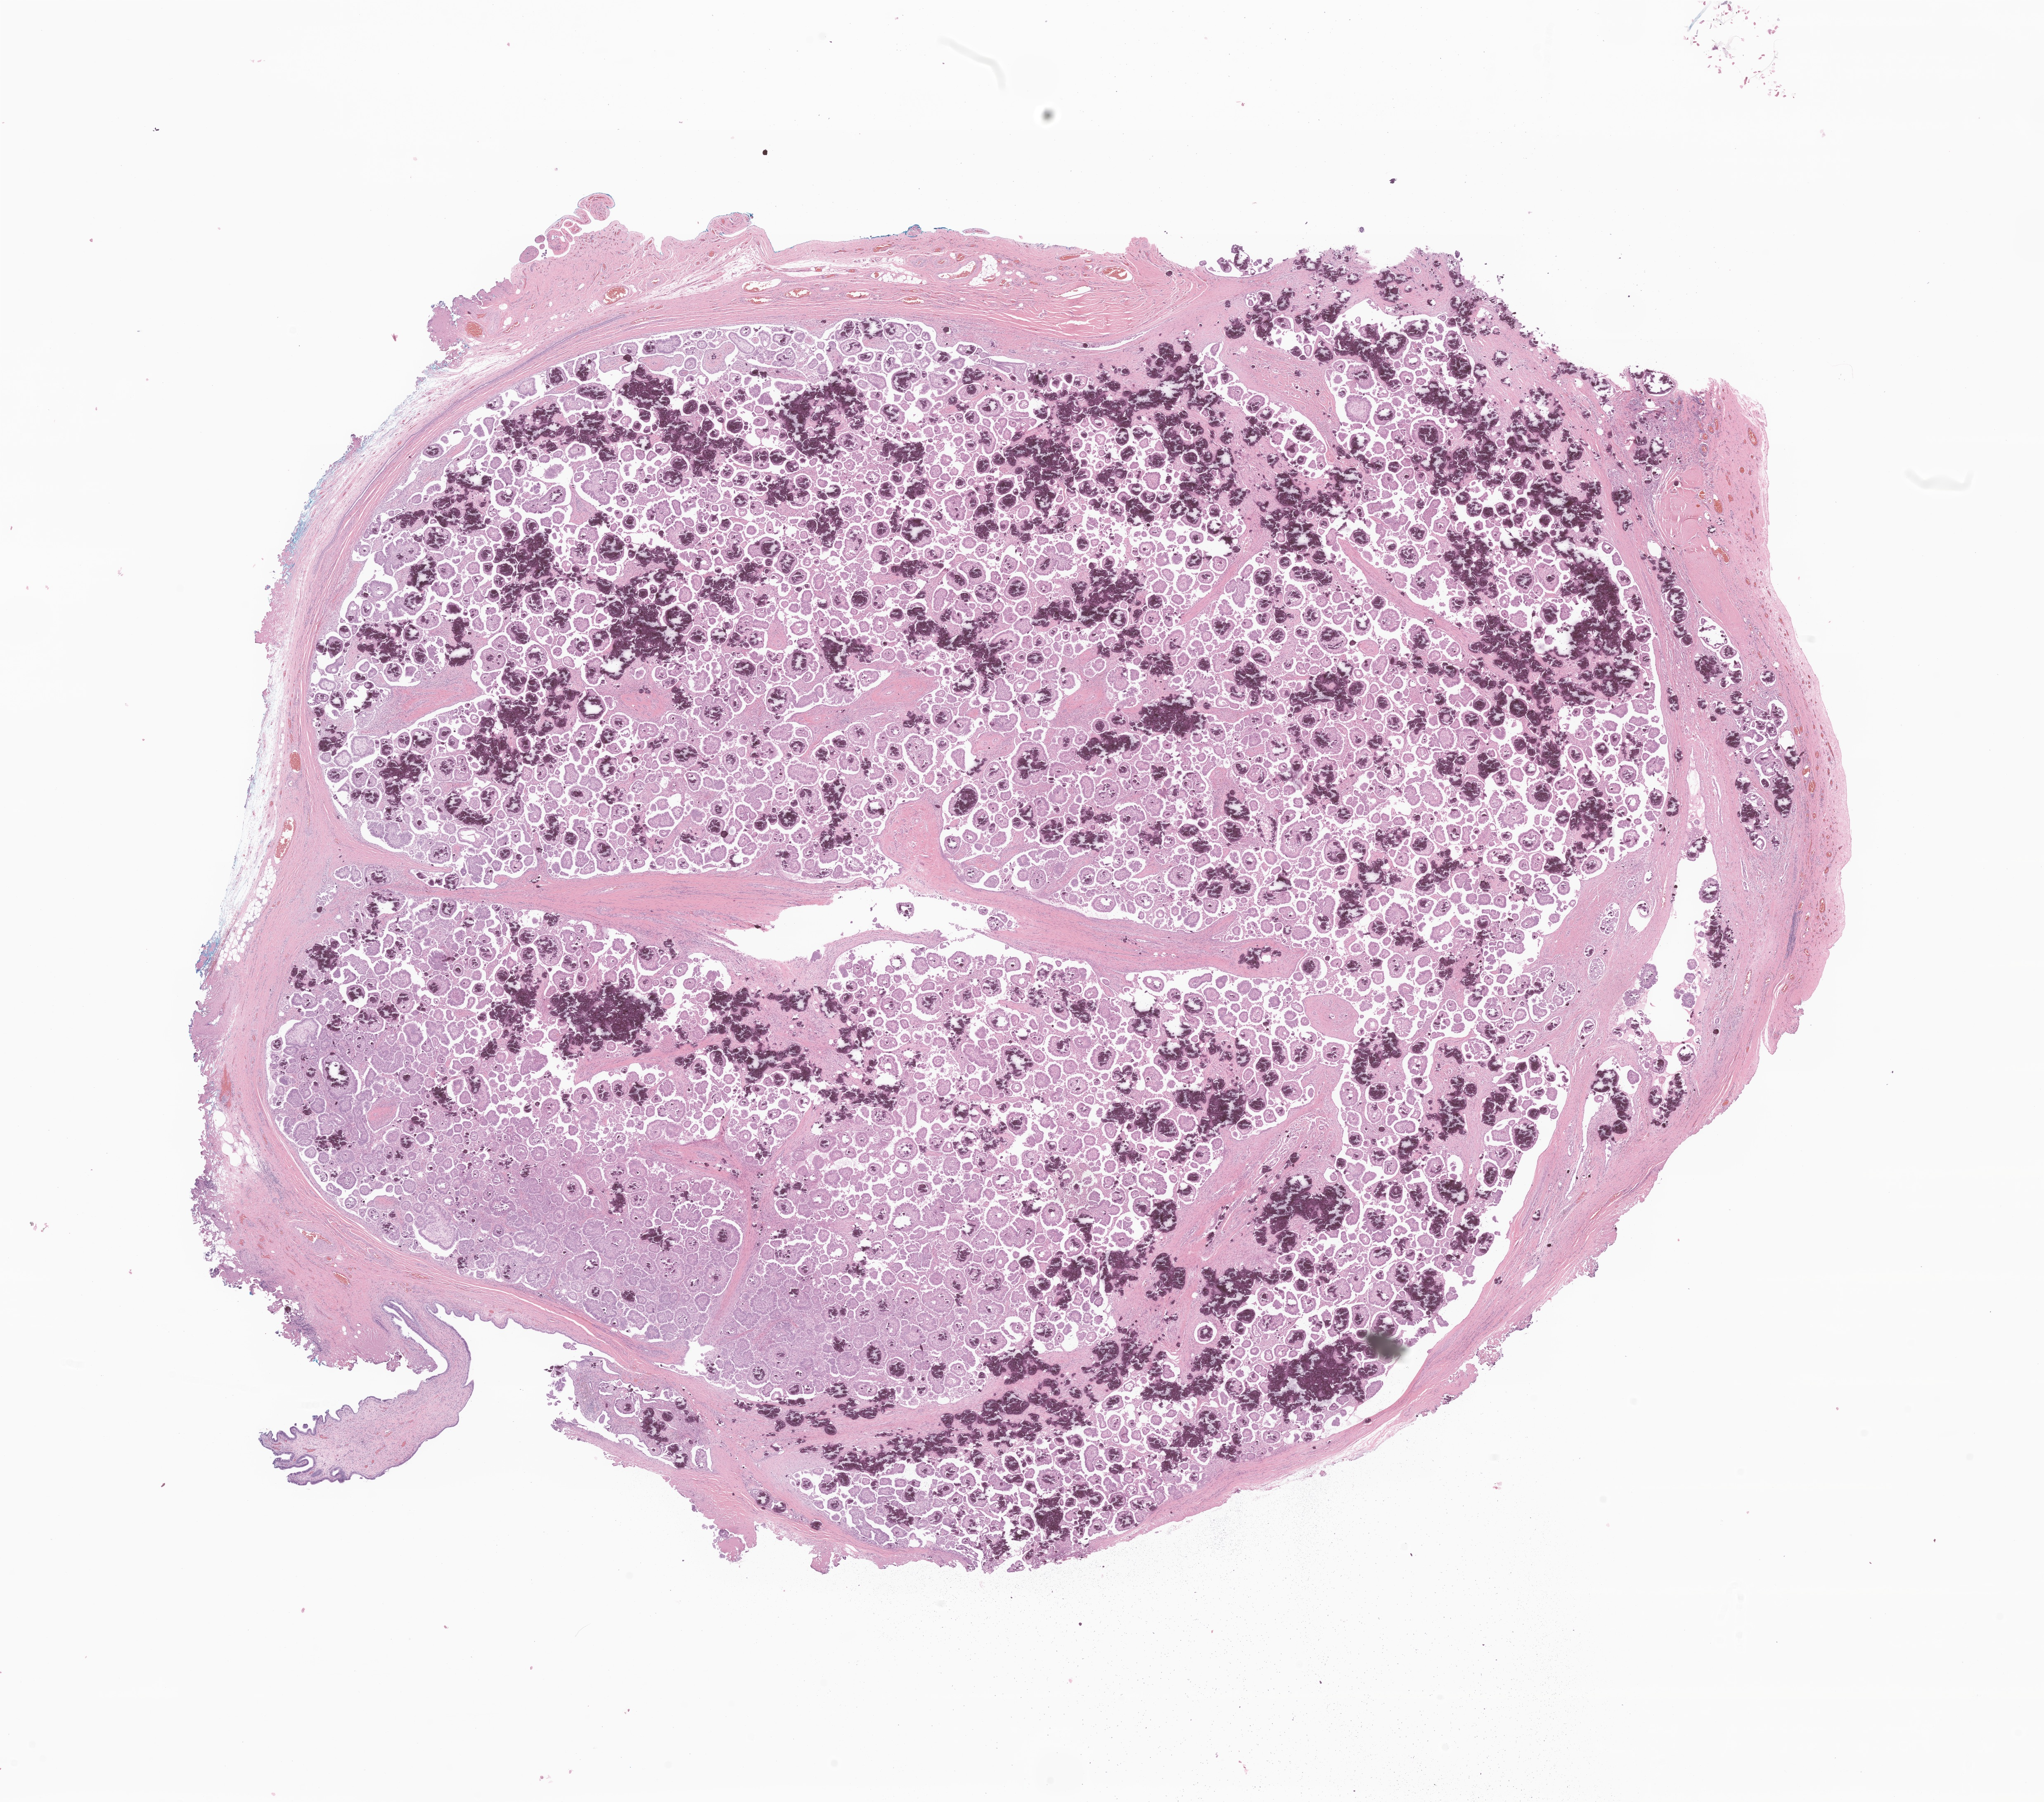
Digitized H&E-stained section of tumor tissue from the epididymis — whole scanned area (about 20.9 x 18.4 mm) shown as a low-resolution overview, formalin-fixed paraffin-embedded section. Patient: male, age 191 months.
Recorded diagnosis: Carcinoma, NOS.